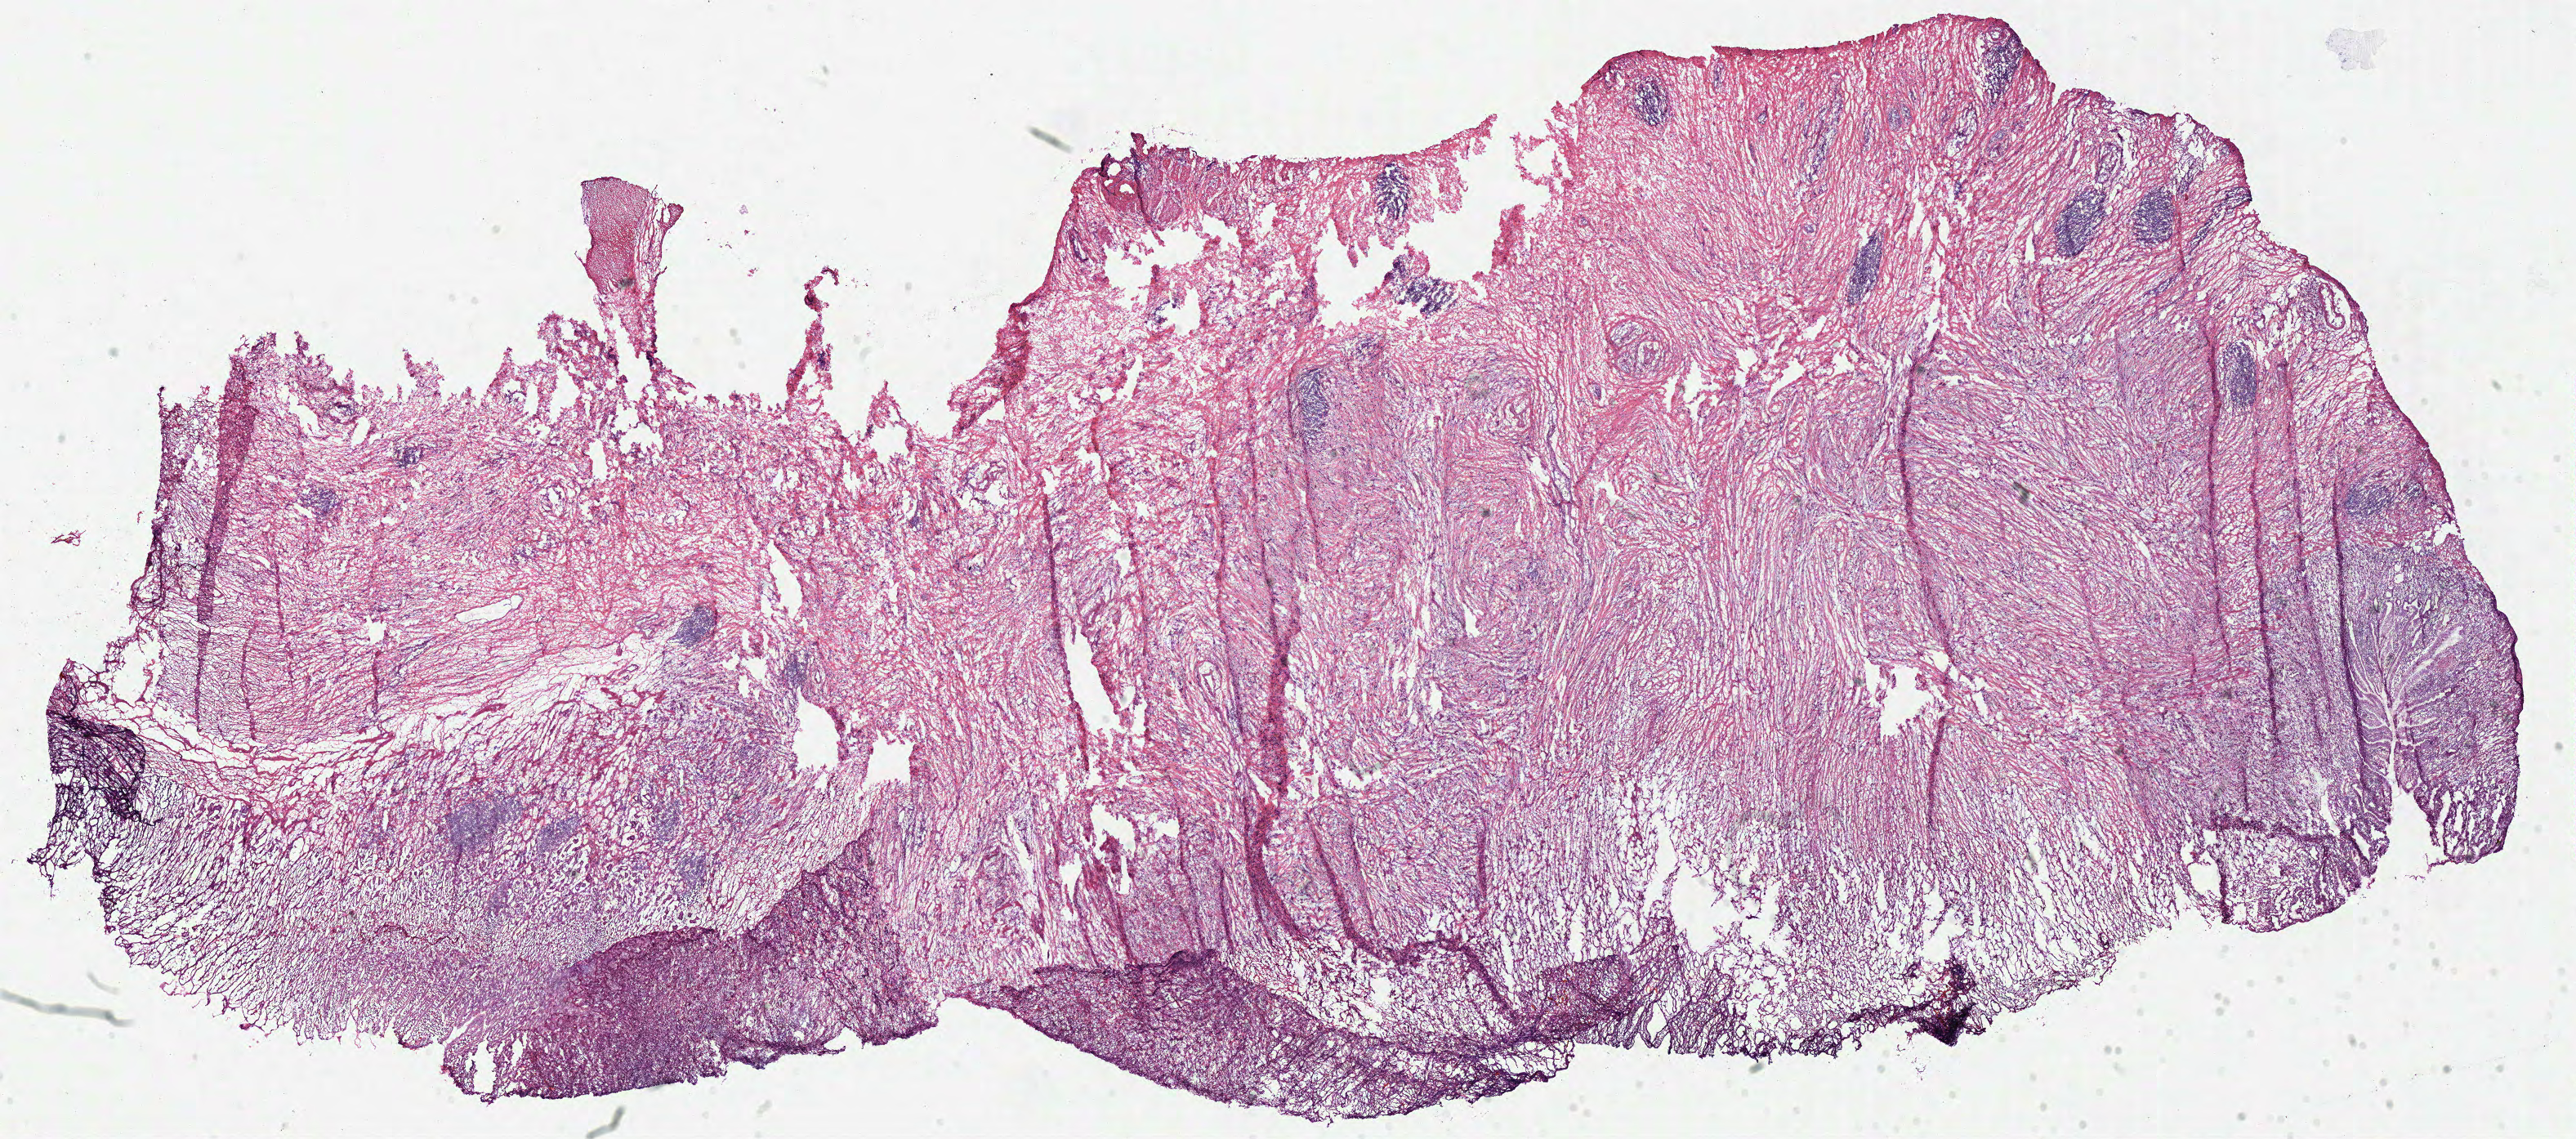
H&E-stained whole-slide image — whole scanned area (about 24.8 x 11.0 mm, from a 40x scan) shown as a low-resolution overview. Frozen section. Stomach, primary tumour sample. Patient: male, age at initial diagnosis 60 years. Histologic grade: G3 (poorly differentiated). Slide review estimates, as recorded: tumour cells 65%, tumour nuclei 70%, normal cells 5%, stromal cells 30%, necrosis 0%.
TNM: T3 N1 M0. Histologic diagnosis: Adenocarcinoma, NOS. AJCC pathologic stage: IIB (7th edition).